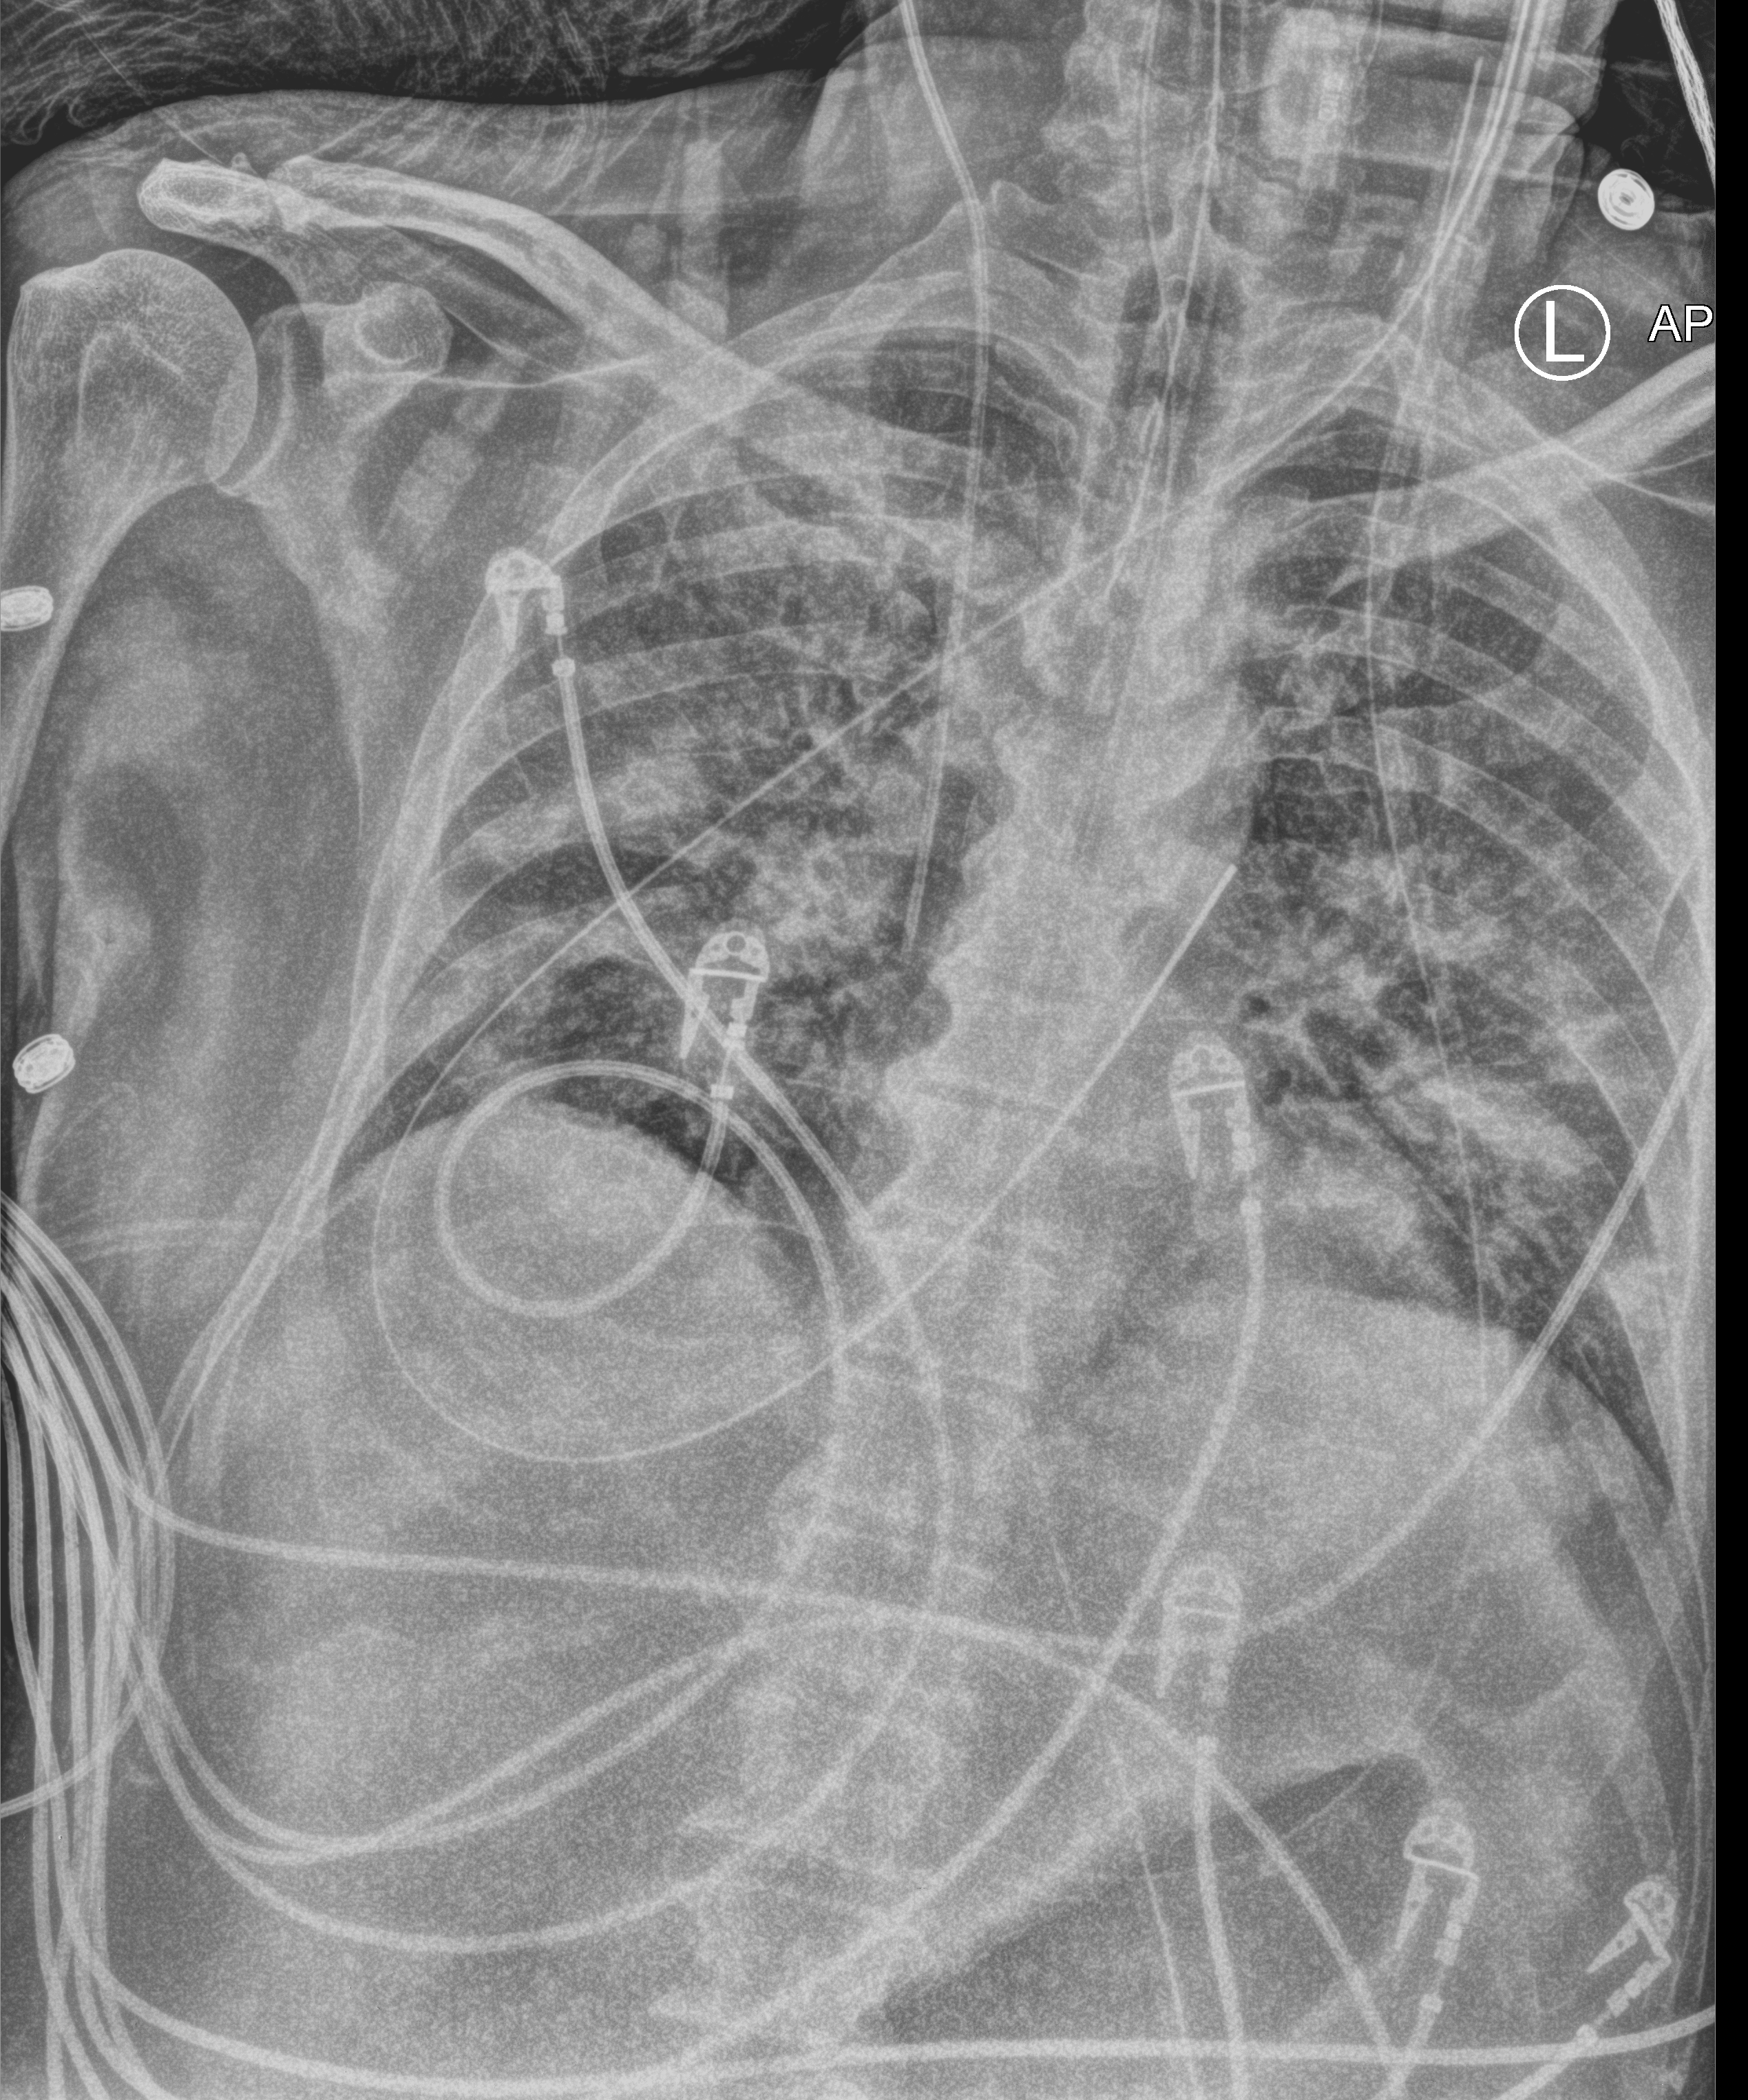
Portable chest radiograph. Patient hospitalised with COVID-19; male, aged 60–74 years.
Hospital-stay facts (about this admission, not read from this image; timing relative to this image not recorded): diabetes (admission record): yes; other chronic lung disease (admission record): no.